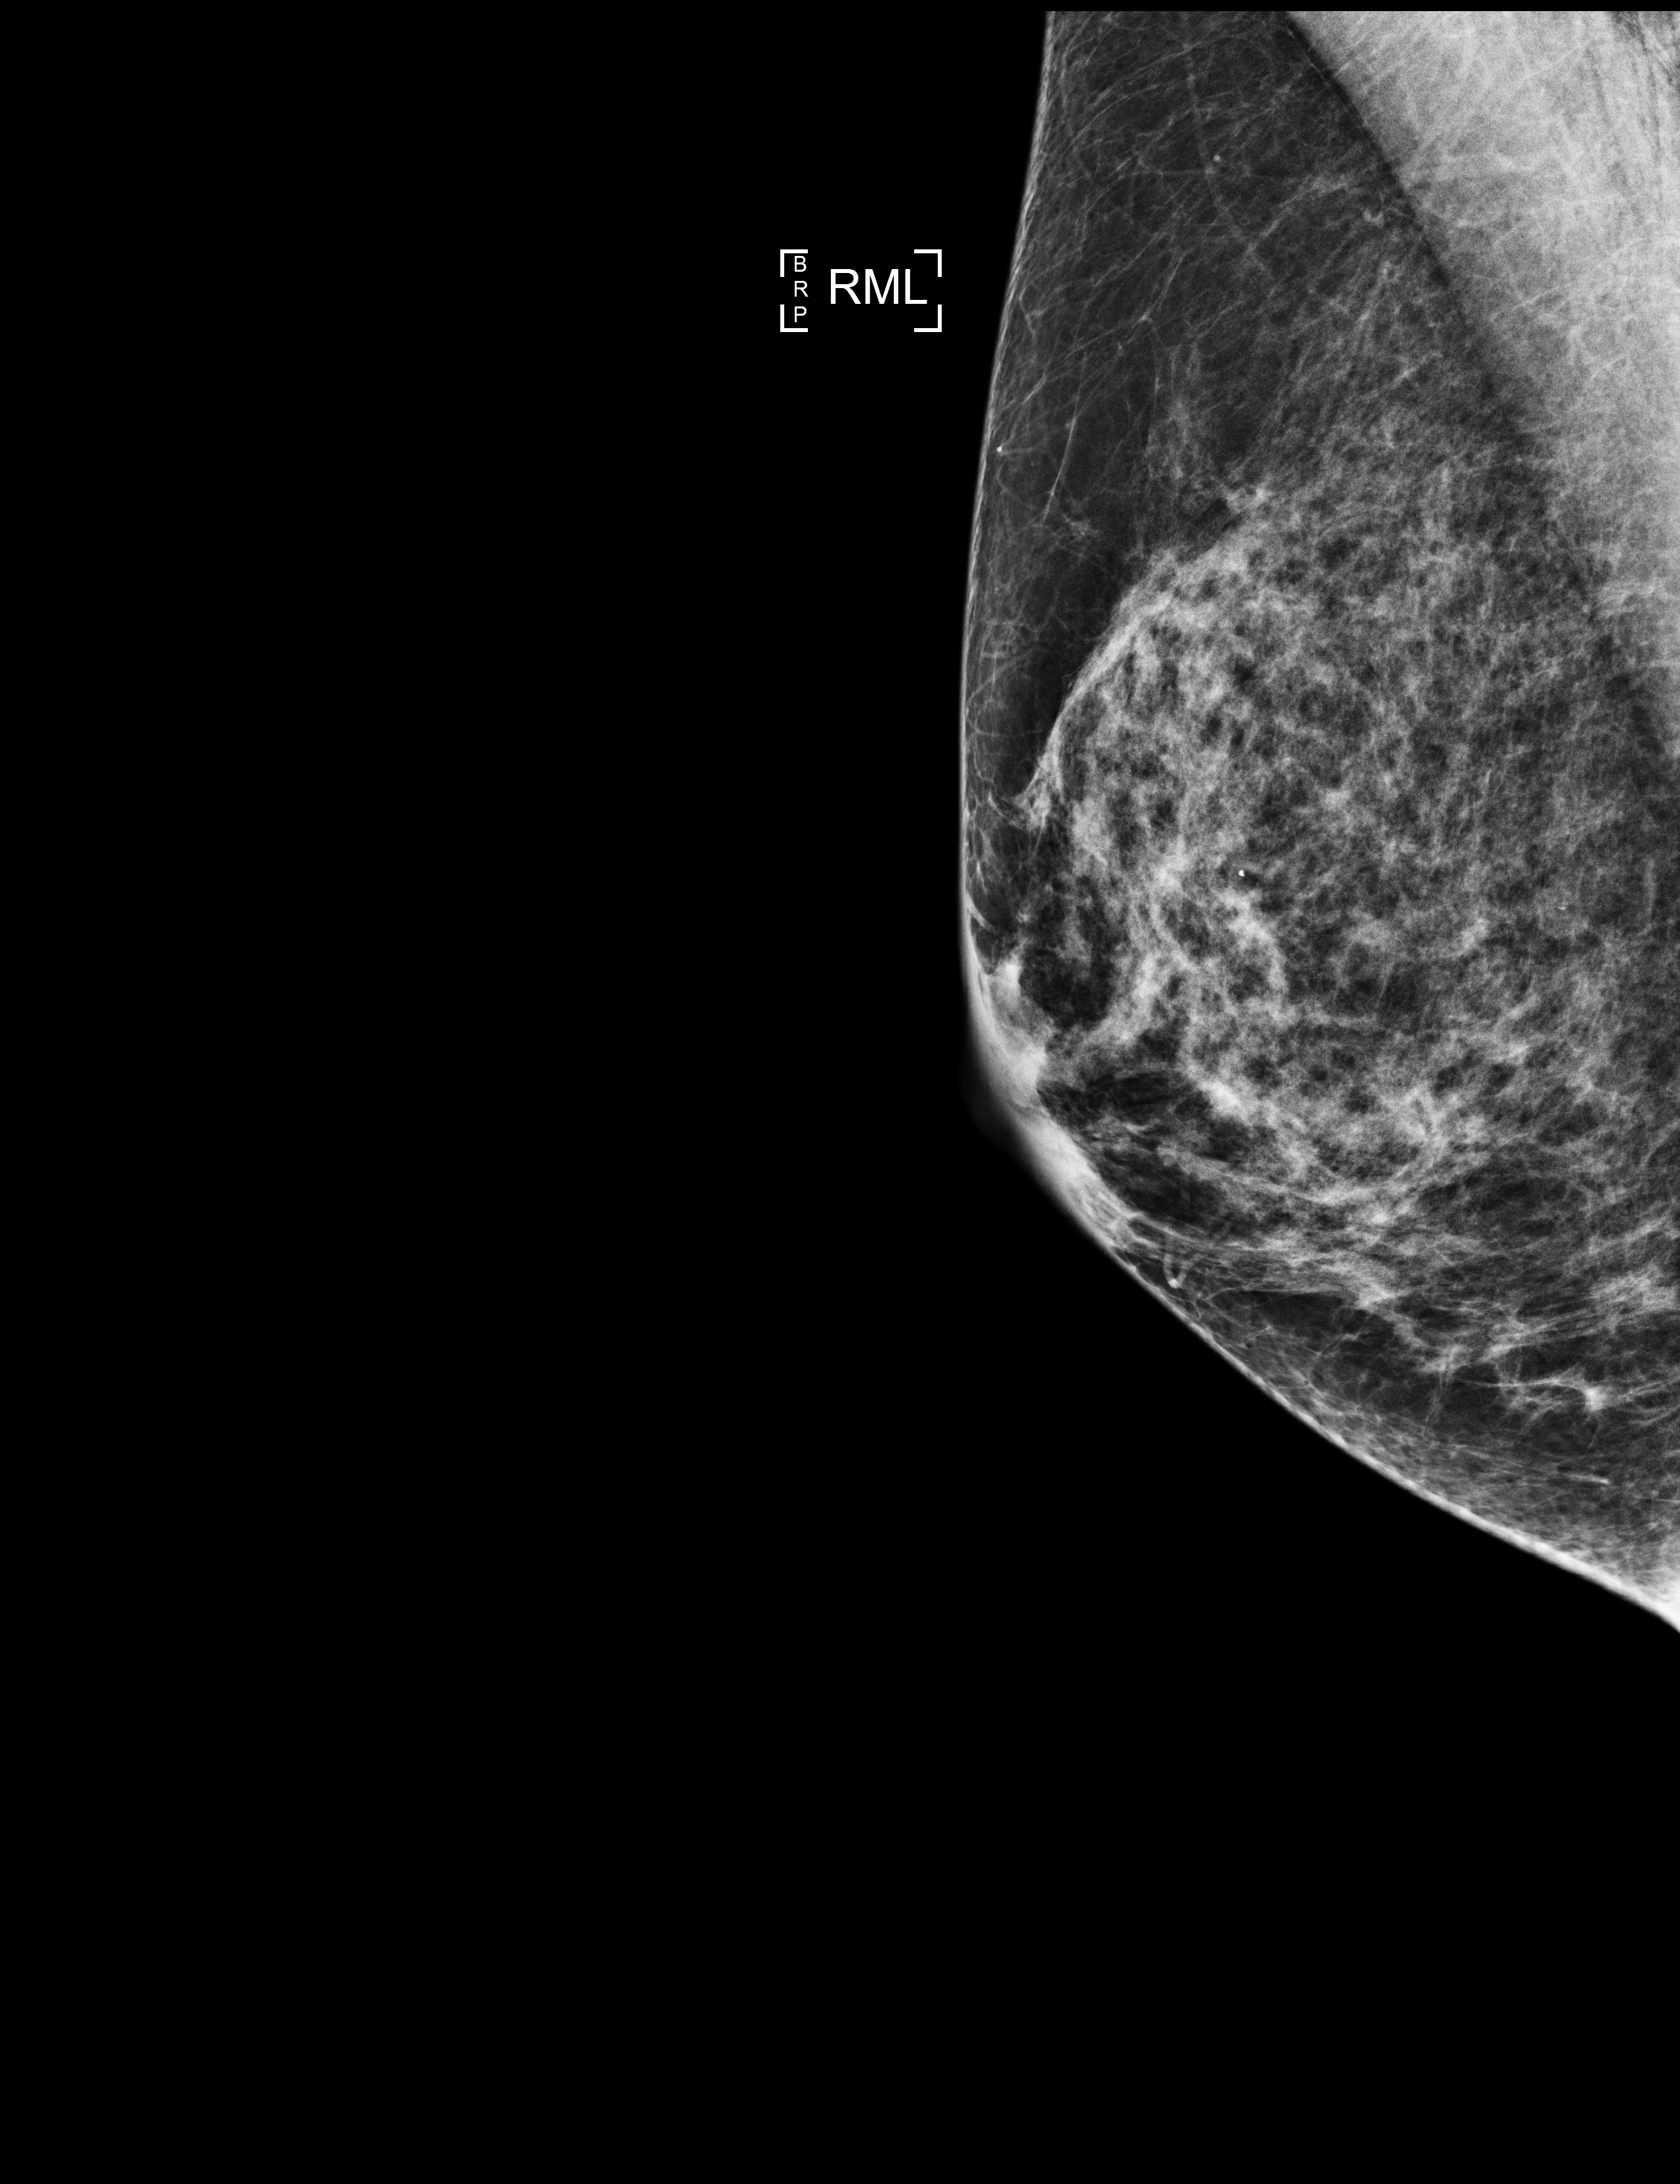
Full-field digital mammogram (FFDM); right breast; ML view; annual screening mammography examination. Female patient, age 63 years.
BI-RADS breast density category at the screening exam (both breasts, scale 1–4): 3. Final BI-RADS assessment for this screening round (tomosynthesis exam, both breasts): category 2. Recall: no recall after this screen.